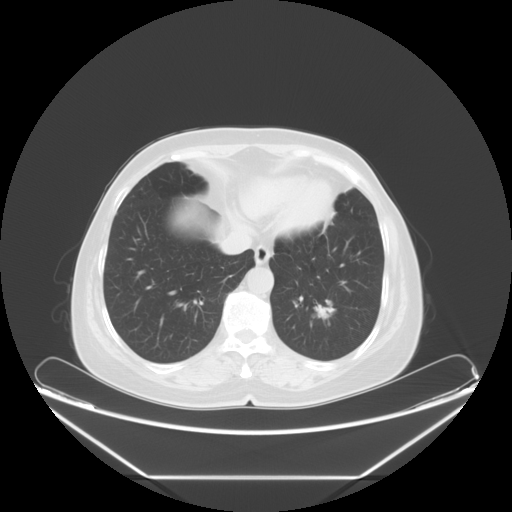
Chest CT, one axial slice. Position 18 of 61 along the scan axis. Reconstruction kernel STANDARD. Lung window (W 1500 / L -600 HU). 5 mm slice thickness. 512 × 512 image matrix, field of view 451 × 451 mm. Patient: female, 63 years. Case-level facts recorded for this patient, not image findings: clinical TNM (as recorded): T1c N0 M0; histopathological grade: G2-3.
Outlined on this slice (rectangle marked by the reading radiologist):
- lung tumour (recorded histology: adenocarcinoma): bounding box (x1, y1, x2, y2) in pixels: (305, 296, 341, 332)